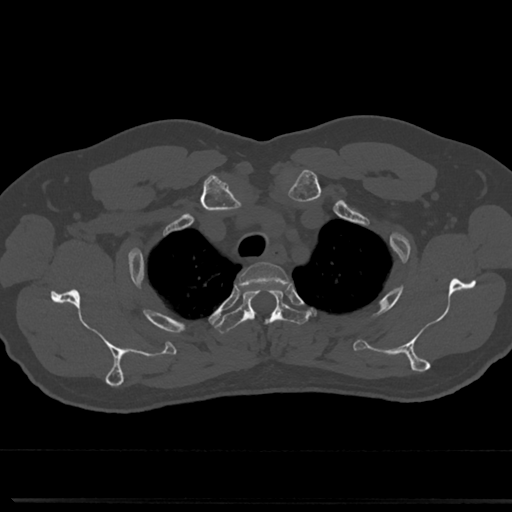
CT including the spine, one axial slice; position 605 of 817 along the scan axis; reconstruction kernel Br40s/3; bone window (W 1800 / L 400 HU); 0.5 mm slice thickness; 512 × 512 image matrix, field of view 355 × 355 mm. Patient: male, 61 years. Case-level facts recorded for this patient, not image findings: primary cancer: prostate.
Annotated regions visible in this slice (semi-automatically segmented with operator editing):
- T2 vertebra: bounding box [x1, y1, x2, y2] px = [240, 262, 288, 283]
- T3 vertebra: [216, 285, 303, 332]